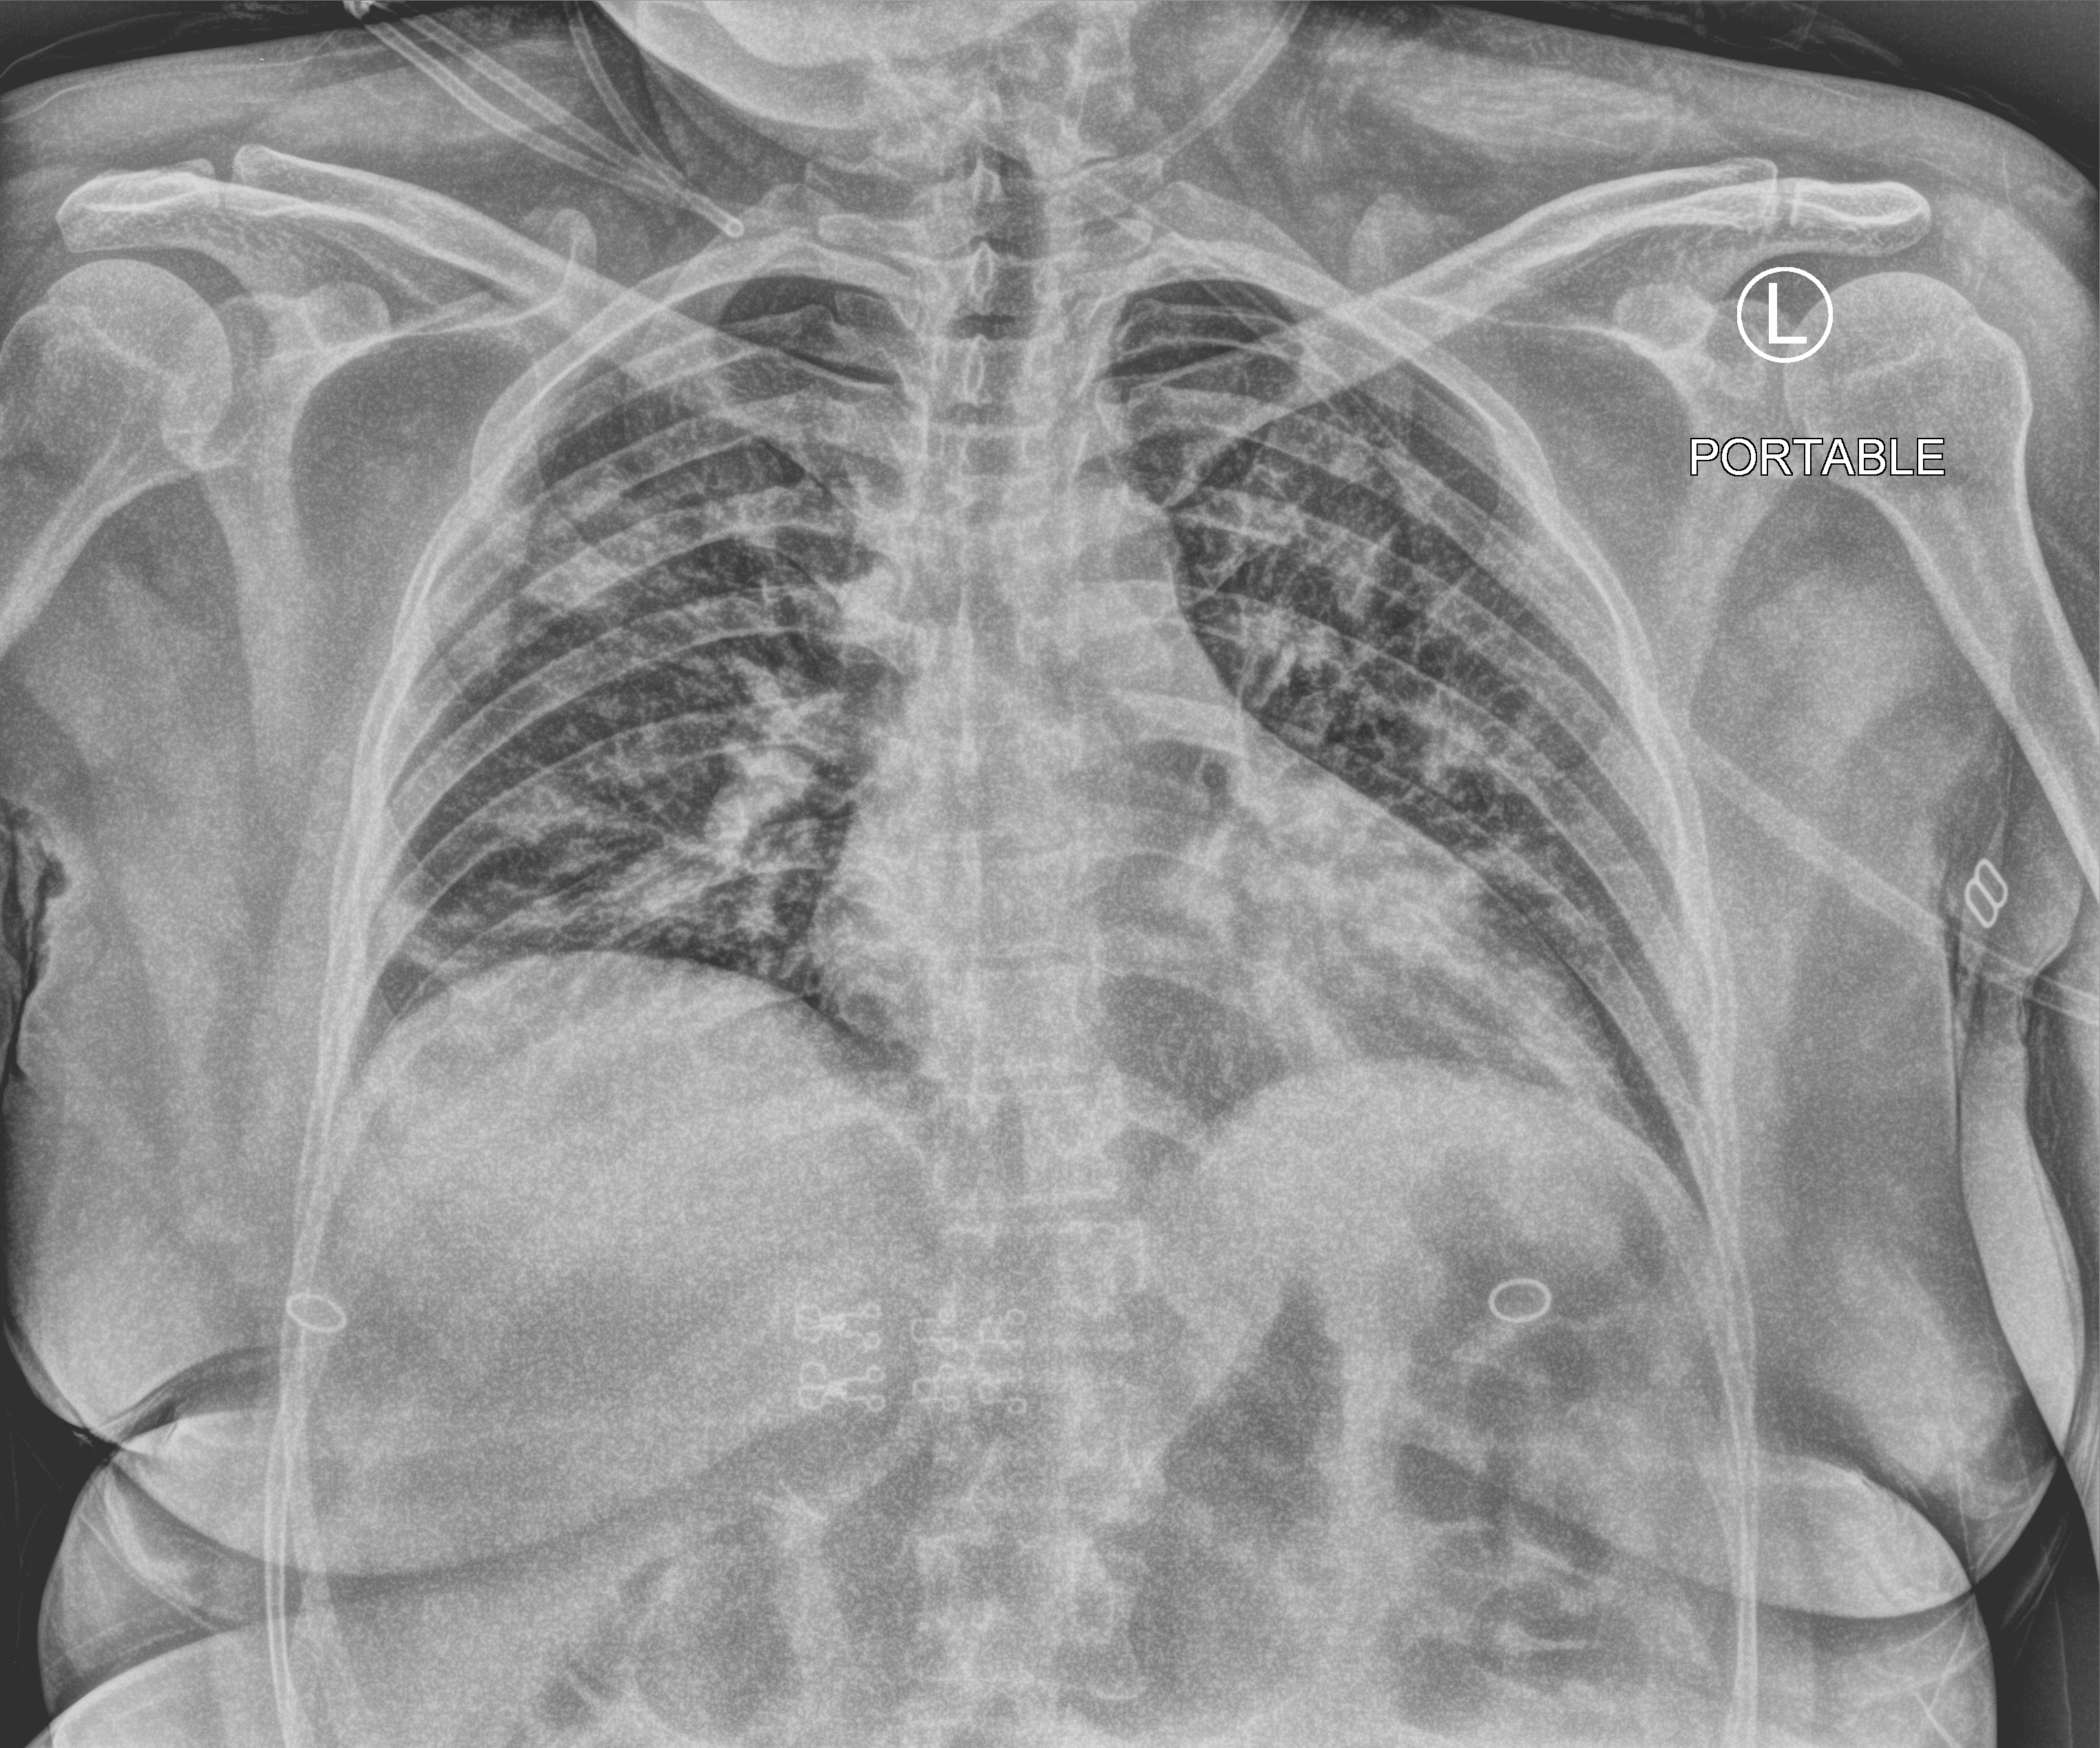
Chest X-ray (portable). Patient hospitalised with COVID-19; female, aged 18–59 years.
Admission-level facts for this patient (not findings on this image; timing relative to this image not recorded):
- mechanically ventilated during this hospital stay: yes
- length of hospital stay: 22 days
- chronic kidney disease (admission record): no